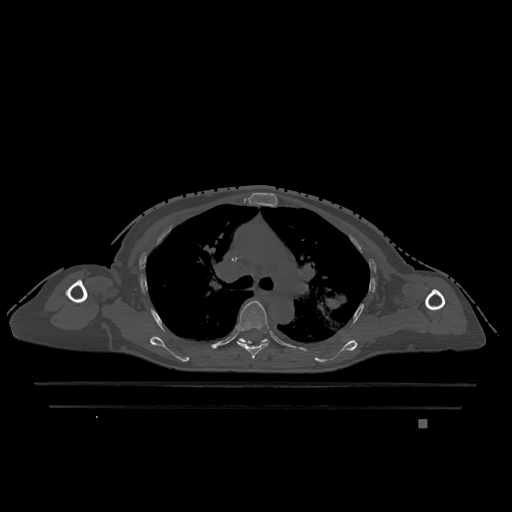
CT including the spine, one axial slice; slice 824 of 1317 in the series (ordered by position); bone window (W 1800 / L 400 HU); 512 × 512 image matrix, field of view 500 × 500 mm. Female patient, age 74 years. From the clinical record (not read from this slice): primary cancer: lung; vertebrae with lytic lesions (as recorded): T1, T4, T5, T6, L4, L5.
Outlined on this slice (semi-automatic segmentation, software-assisted and operator-edited):
- T5 vertebra: bounding box [x1, y1, x2, y2] px = [237, 300, 270, 359]
- T6 vertebra: [238, 338, 268, 344]